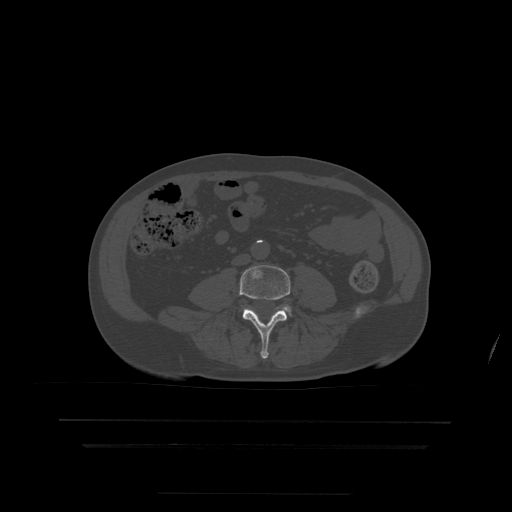
CT including the spine, one axial slice. Slice 92 of 522 in the series (ordered by position). Bone window (W 1800 / L 400 HU). 512 × 512 image matrix, field of view 436 × 436 mm. Patient age 68 years. Case-level facts recorded for this patient, not image findings: primary cancer: urothelial.
Annotated regions visible in this slice (semi-automatically segmented with operator editing):
- L4 vertebra: bounding box <239,266,291,359> (left, top, right, bottom; pixels)
- L5 vertebra: <283,306,291,312>